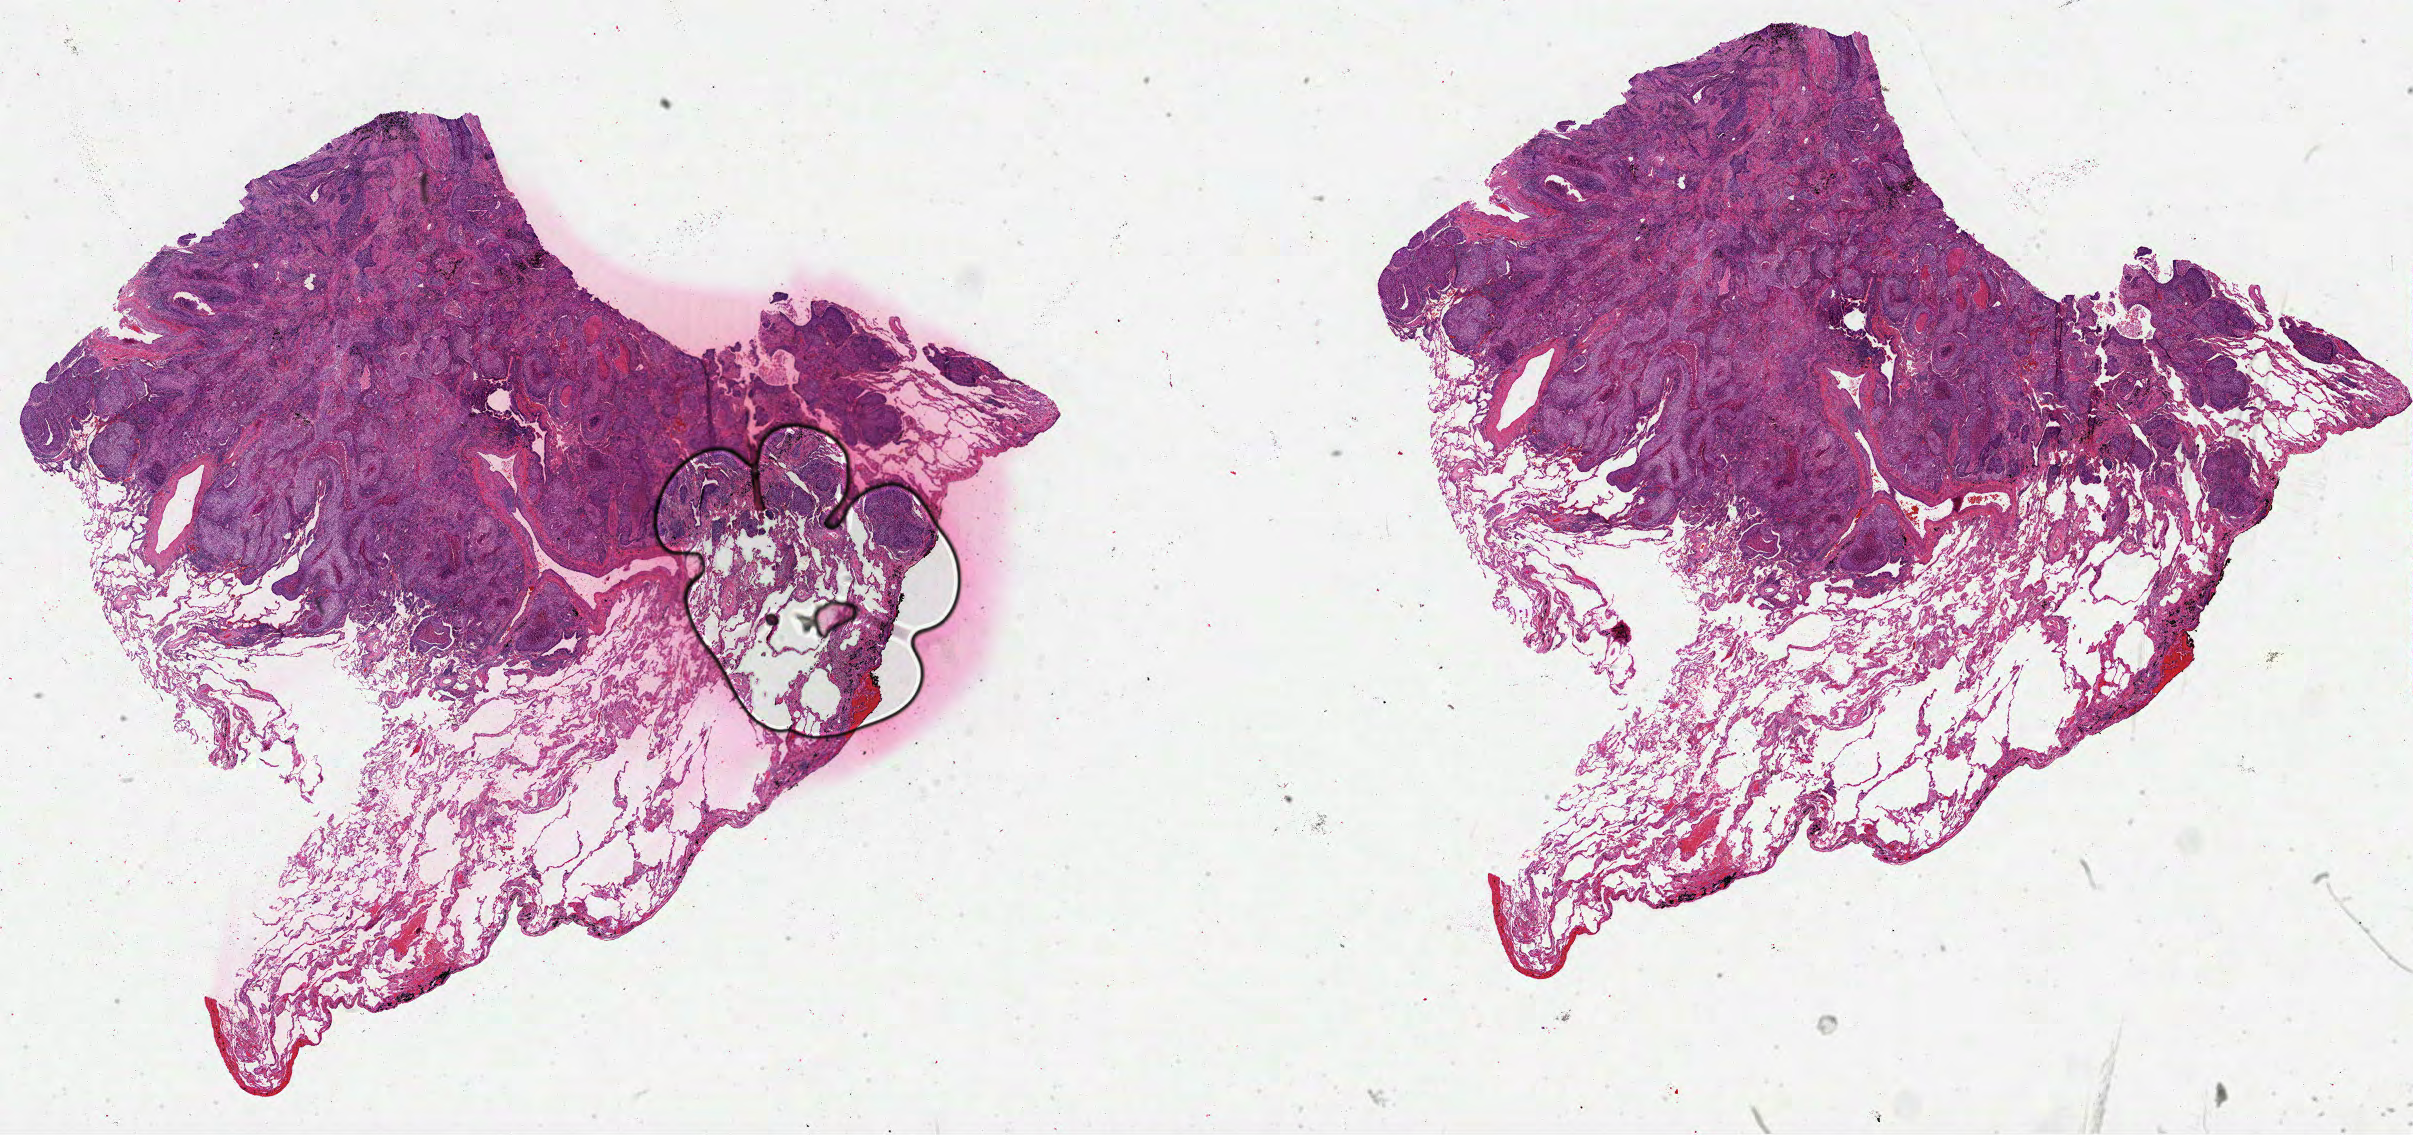
Digitized H&E-stained tissue section (whole slide) — whole scanned area (about 38.9 x 18.3 mm) shown as a low-resolution overview; formalin-fixed paraffin-embedded (FFPE) diagnostic section; primary tumour sample from the lung. Female patient; age at initial diagnosis 76 years.
AJCC pathologic stage: IB. Histologic diagnosis: Squamous cell carcinoma, NOS.